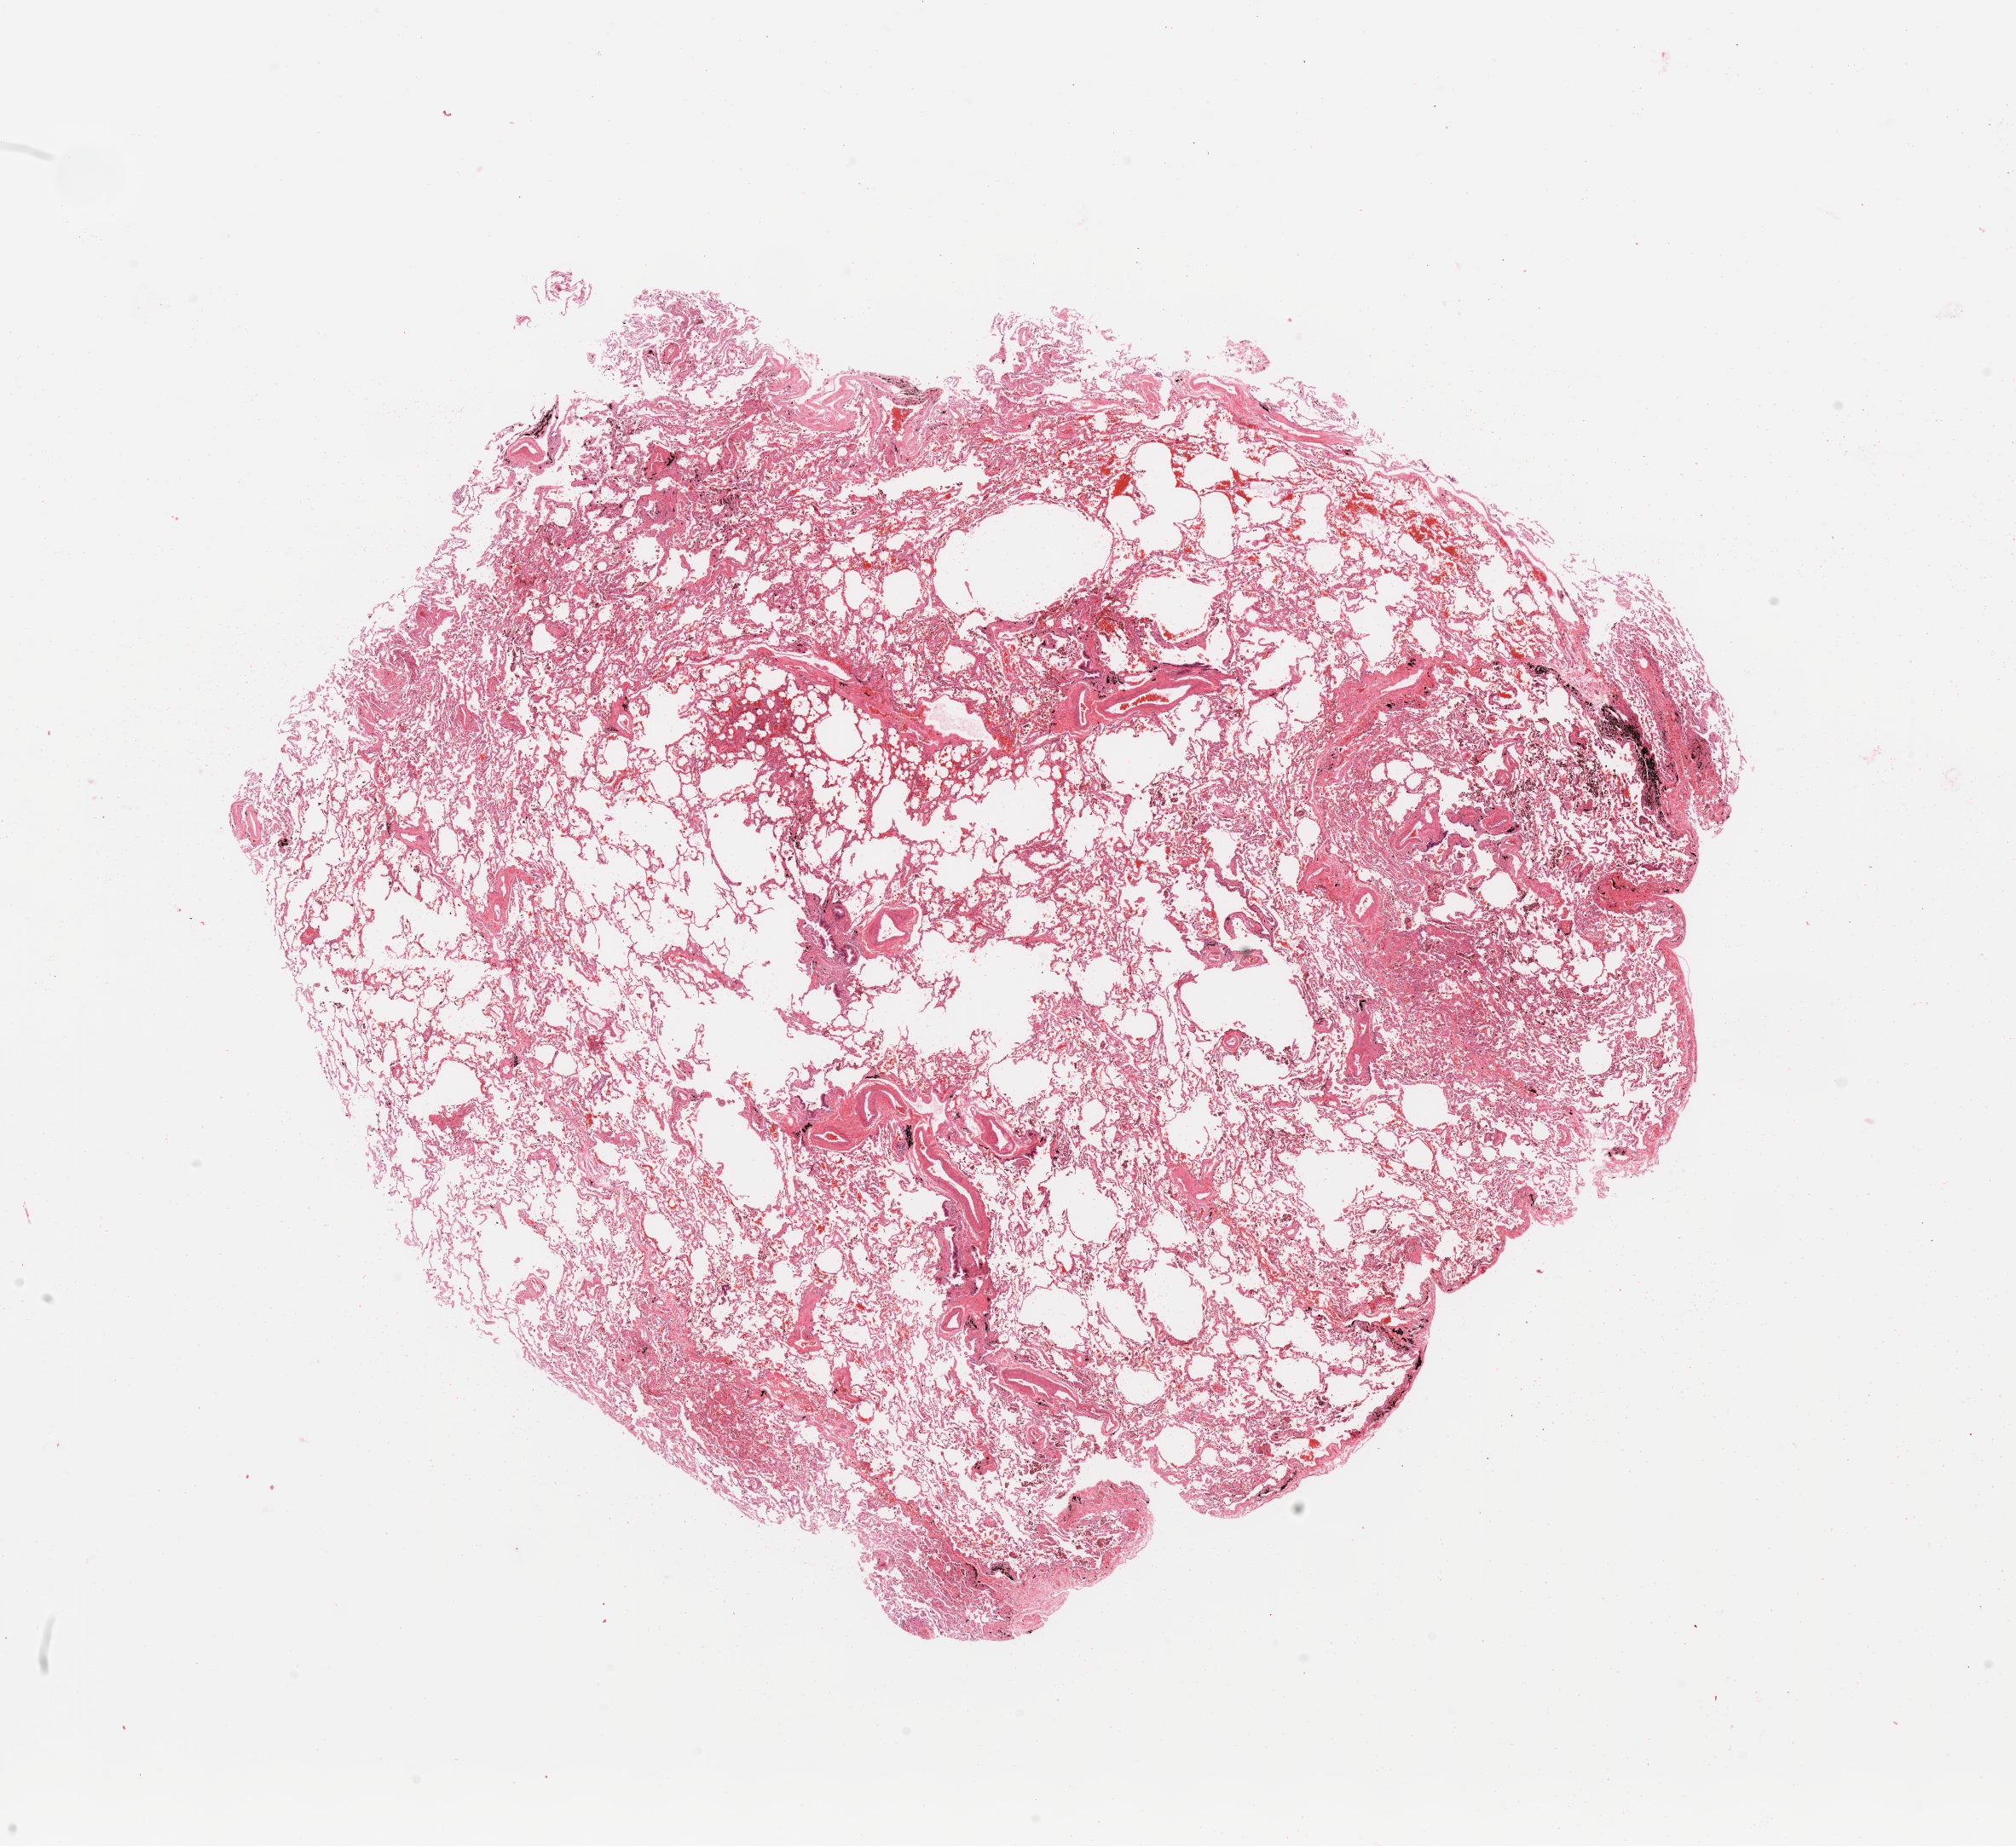
Whole-slide histology image, H&E — whole scanned area (about 18.7 x 17.1 mm) shown as a low-resolution overview, normal (non-tumour) tissue sample, sampled site: lung. Patient: male, age 59 years.
This section: normal (non-tumour) tissue from the same patient. Patient diagnosis: Adenocarcinoma, NOS.